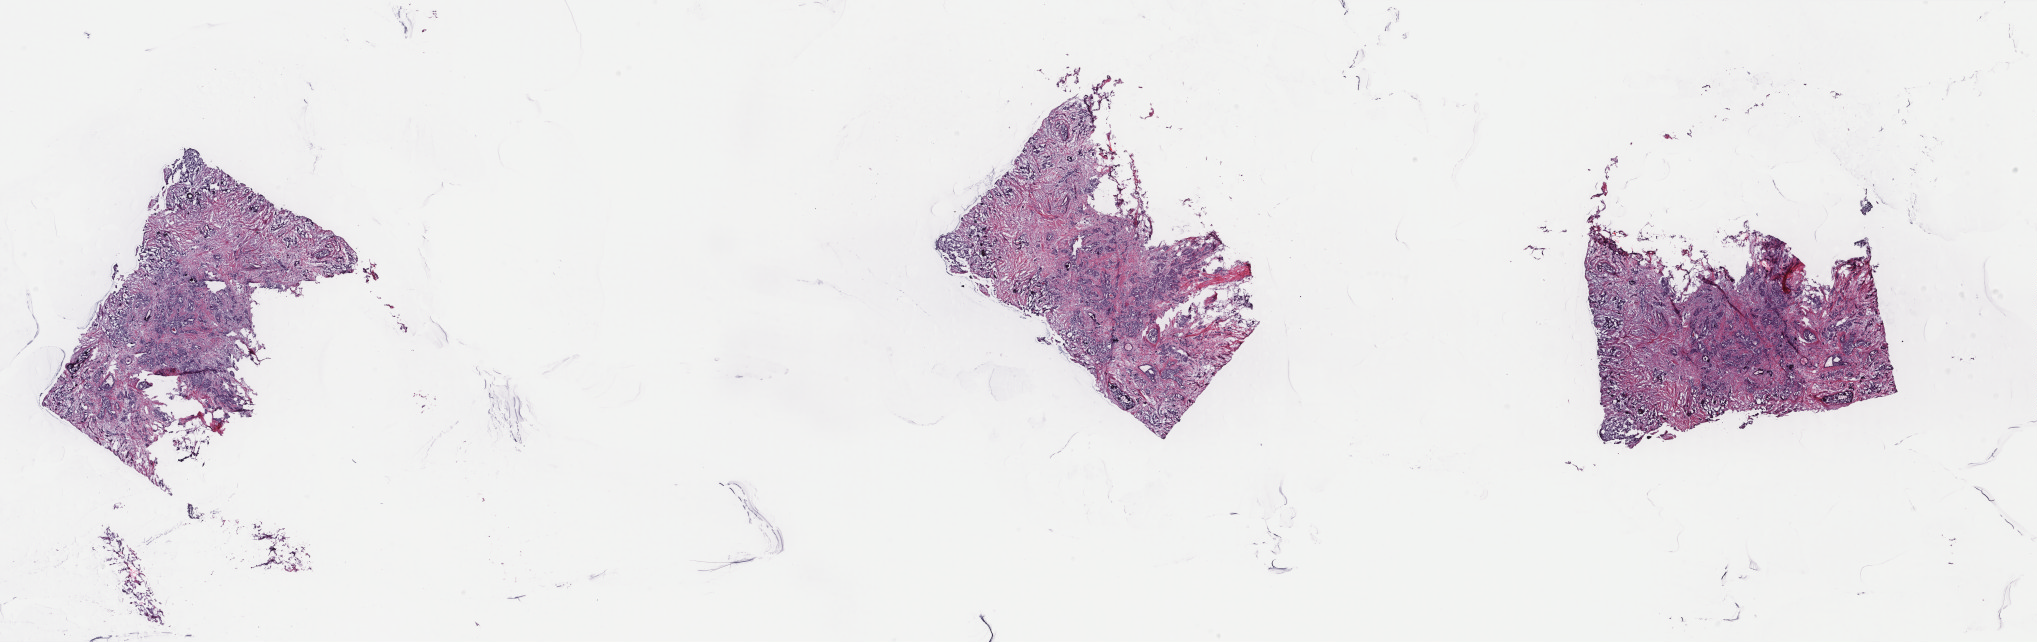
Digitized H&E-stained tissue section (whole slide), low-resolution overview of the scanned area, about 32.3 x 10.2 mm. Frozen section. Primary tumour sample from the breast. Patient: female, age at initial diagnosis 57 years. Pathologist review of this section (percent, as recorded): tumour cells 35%, tumour nuclei 80%, normal cells 8%, stromal cells 55%, necrosis 2%. Inflammatory infiltration, as recorded: lymphocyte infiltration 1%, monocyte infiltration 0%, neutrophil infiltration 0%.
- laterality: right
- lymph nodes positive (case pathology): 0 of 11 examined
- AJCC pathologic stage: IIA (7th edition)
- histologic diagnosis: Infiltrating duct carcinoma, NOS